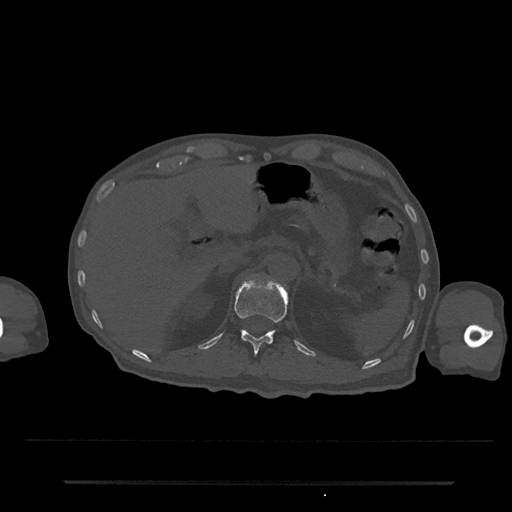
CT including the spine, one axial slice. Slice 188 of 797 in the series (ordered by position). Reconstruction kernel Br40s/3. Bone window (W 1800 / L 400 HU). 512 × 512 image matrix, field of view 427 × 427 mm. Patient: male, 74 years. Case-level facts recorded for this patient, not image findings: primary cancer: prostate.
Structures marked on this image (semi-automatic segmentation, software-assisted and operator-edited):
- T12 vertebra: box from (x=234, y=280) to (x=288, y=355) px